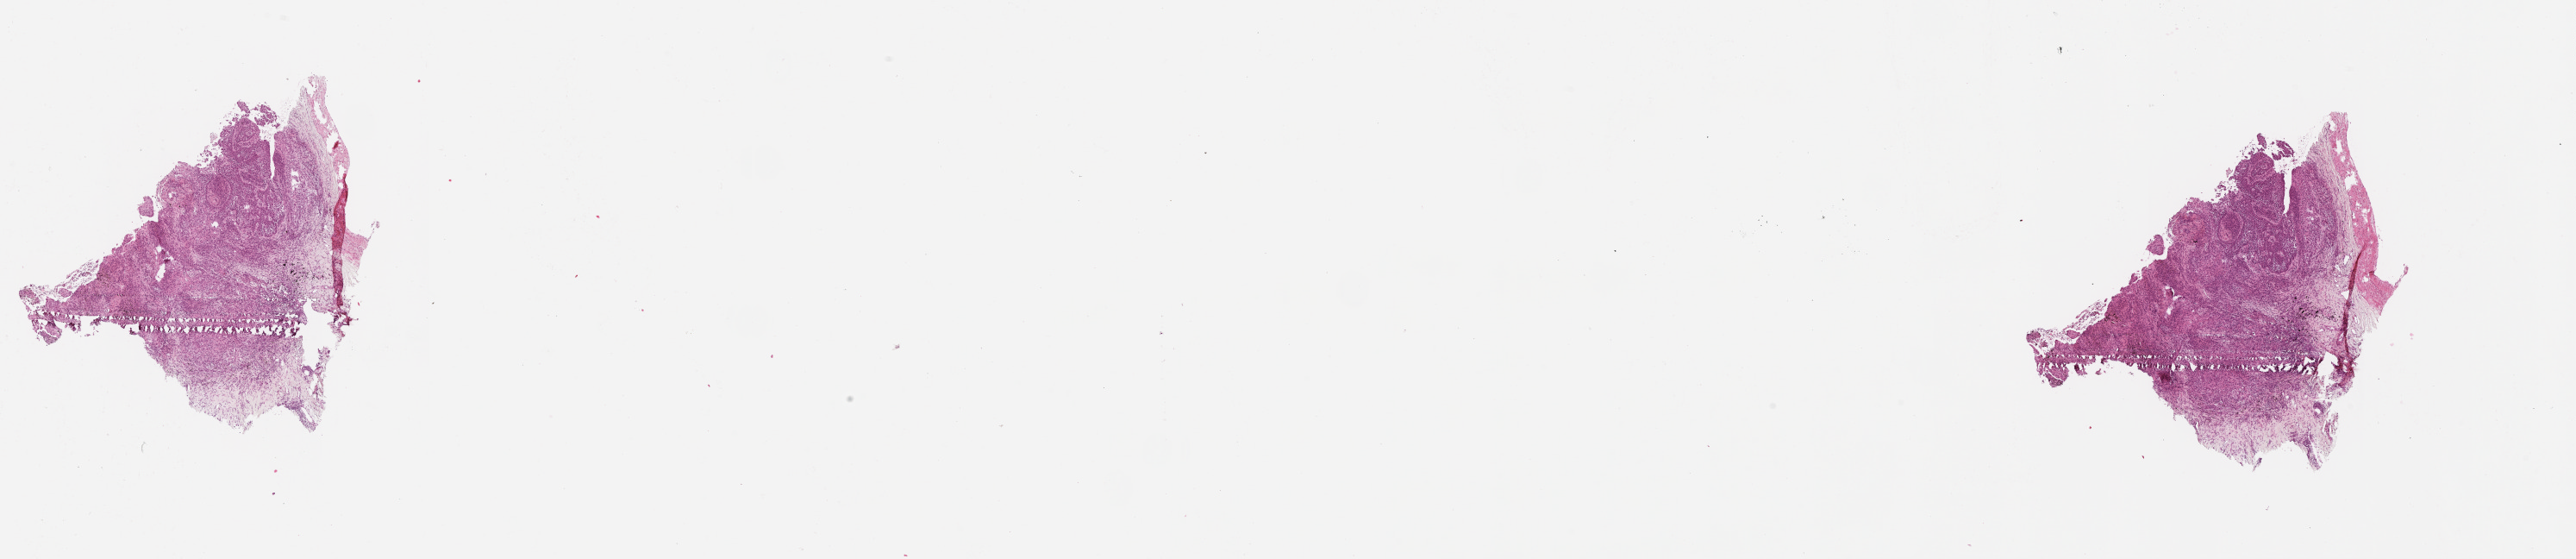
H&E-stained whole-slide image, whole scanned area (about 24.1 x 5.2 mm) shown as a low-resolution overview, tumour tissue sample, lung. Female, 70 y/o.
* patient diagnosis (cohort enrolment): squamous cell carcinoma (lung)